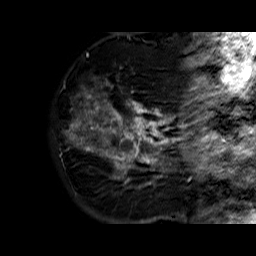
Breast MRI (dynamic contrast-enhanced), one sagittal slice. Slice 16 of 60 in the series (ordered by position). Dynamic contrast-enhanced series, time point 2 of 6 at this slice position (early post-contrast). 1.5 T. TE 6.3 ms, TR 32.4 ms. 4 mm slice thickness. 256 × 256 image matrix, field of view 200 × 200 mm. Female patient. Case-level facts recorded for this patient, not image findings: setting: breast cancer imaged before/during neoadjuvant chemotherapy; receptor status: HR-positive, HER2-negative.
Annotated regions visible in this slice (semi-automatically segmented with operator editing):
- analysis volume of interest (the breast-tissue region the enhancement analysis was run in; not a lesion): bounding box <69,73,177,183> (left, top, right, bottom; pixels)
- tumour enhancement mask (voxels above the 100 % enhancement threshold inside the analysis volume of interest): <79,83,177,183>